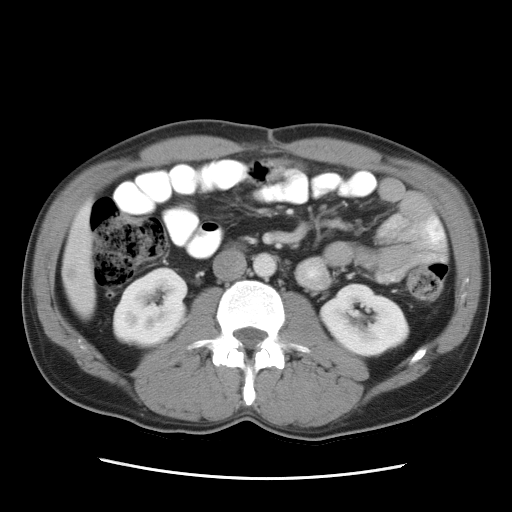
Contrast-enhanced abdominal CT, one axial slice; position 8 of 34 along the scan axis; reconstruction kernel STANDARD; 120 kVp; intravenous contrast given; soft-tissue window (W 400 / L 40 HU); 7.5 mm slice thickness; 512 × 512 image matrix, field of view 360 × 360 mm. Male patient, age 40 years. From the clinical record (not read from this slice): diagnosis: colorectal cancer liver metastases, imaged before liver resection; multiple liver metastases: yes; largest metastasis: 1.5 cm; disease in both lobes: yes.
Annotated regions visible in this slice (outlined manually by an expert reader):
- liver: bounding box (x1, y1, x2, y2) in pixels: (63, 205, 96, 314)
- liver metastasis: (66, 264, 80, 282)